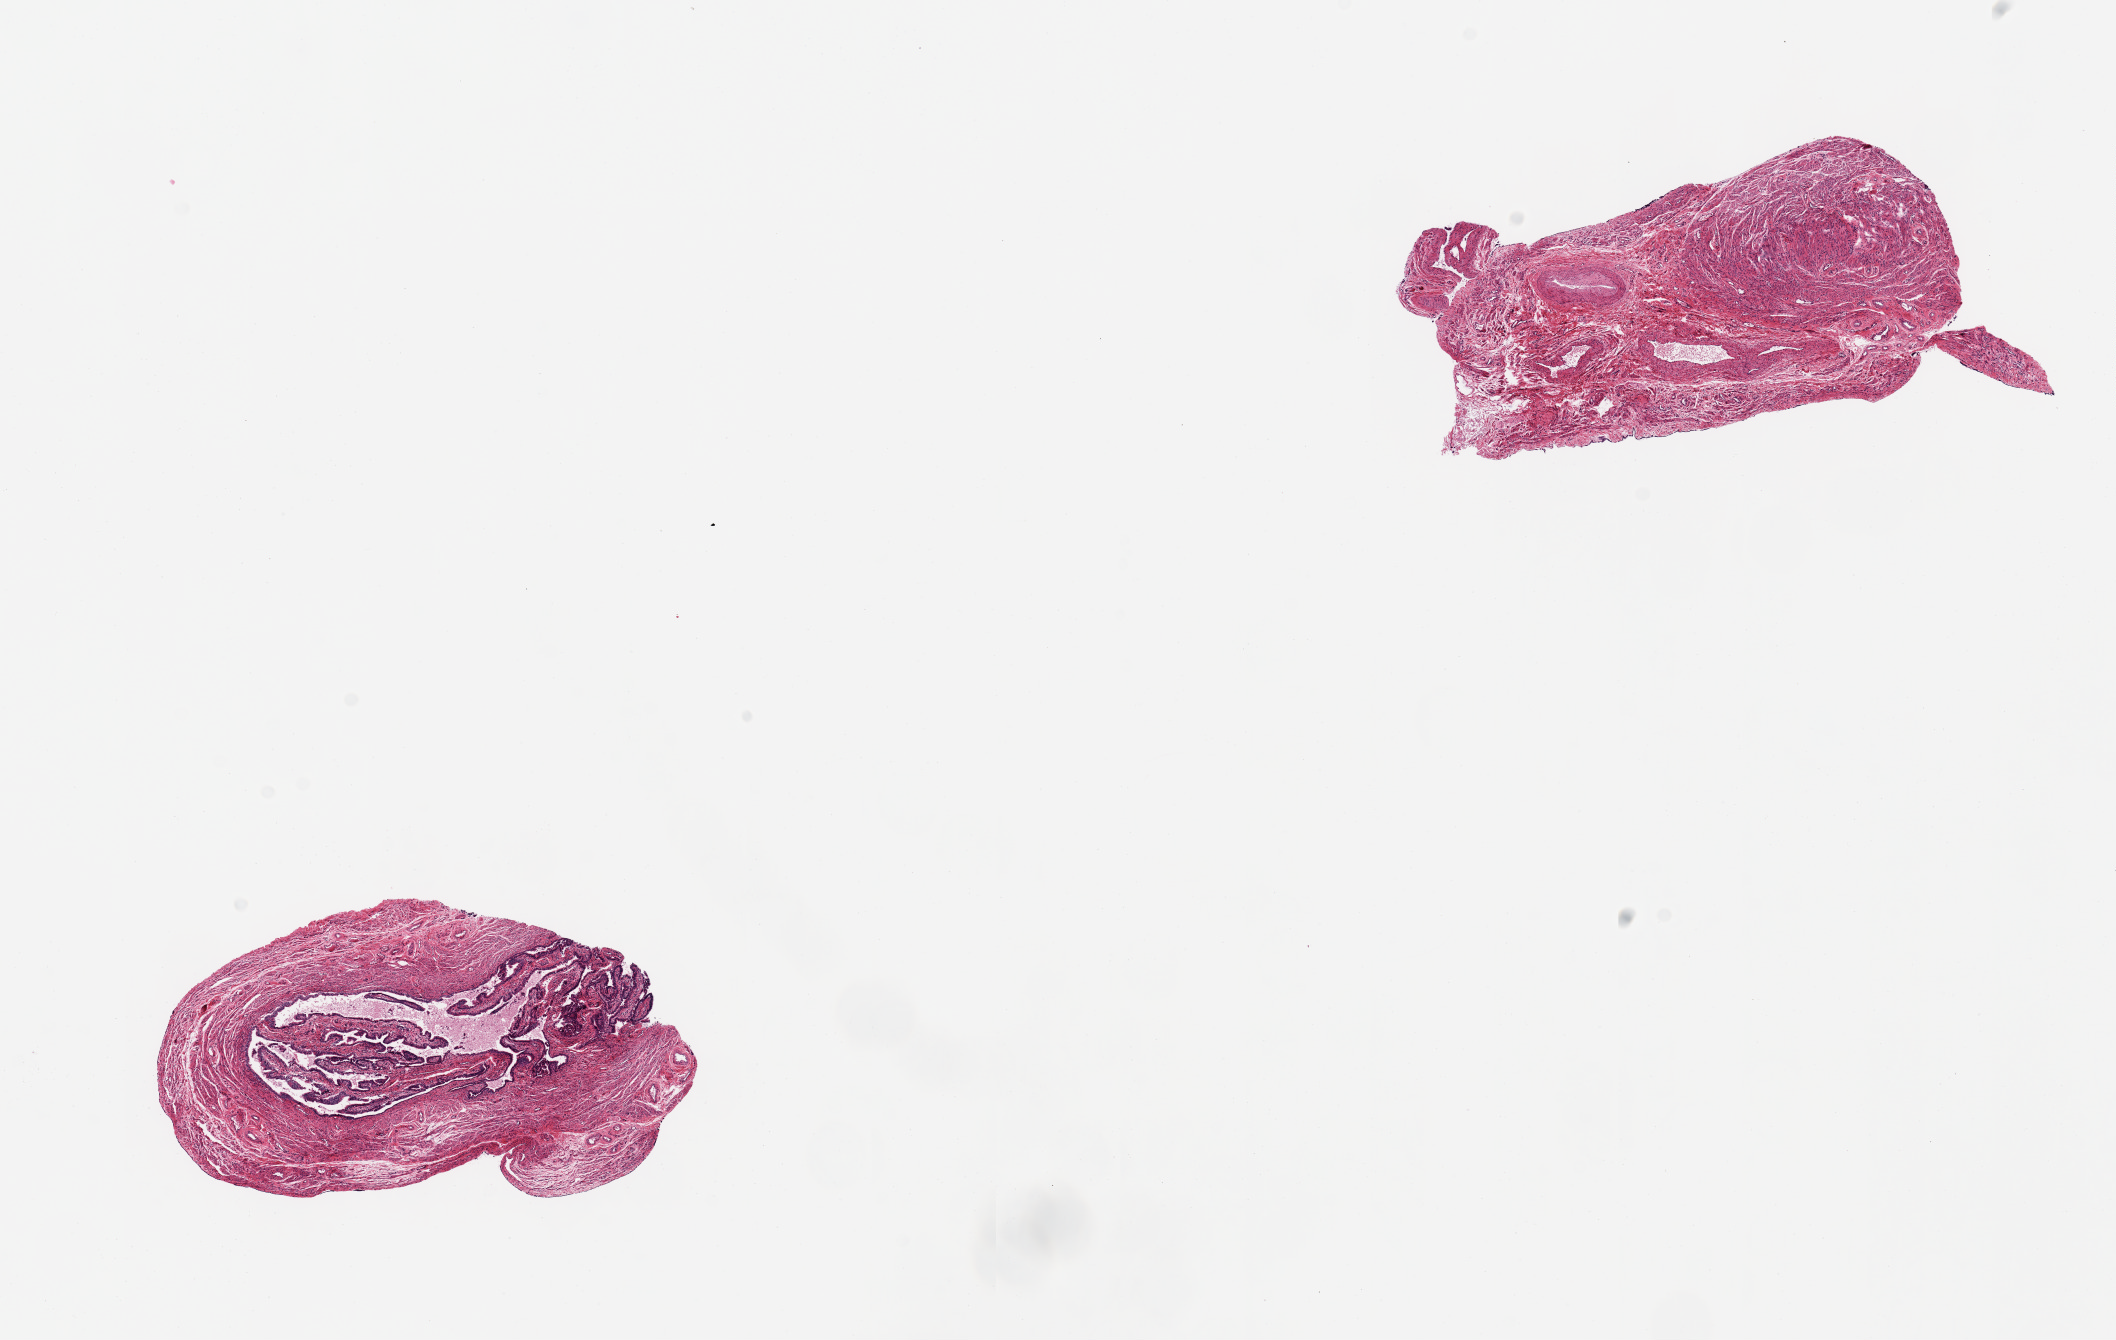
Digitized H&E-stained section — low-resolution overview of the scanned area, about 16.7 x 10.6 mm (acquisition: 20x scan); PAXgene-fixed paraffin-embedded (PFPE) section; target tissue: fallopian tube; tissue donor sample.
Review note (as recorded): 1 4x2mm fallopian tube, good epithelium; one with muscular wall and vessels only.